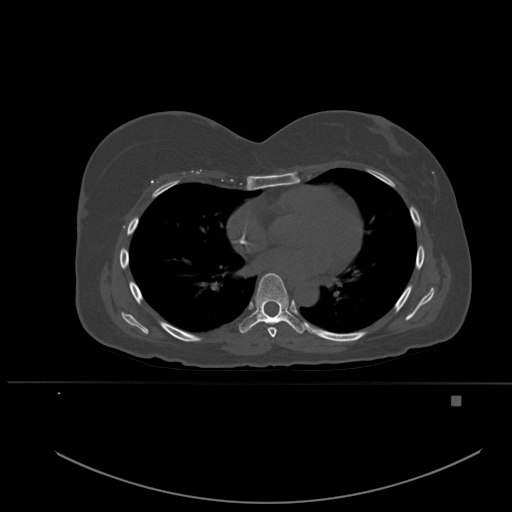
CT including the spine, one axial slice. Position 339 of 651 along the scan axis. Bone window (W 1800 / L 400 HU). 1.5 mm slice thickness. 512 × 512 image matrix, field of view 443 × 443 mm. Female patient, age 49 years. From the clinical record (not read from this slice): primary cancer: breast; vertebrae with lytic lesions (as recorded): L3, T12, L4.
Outlined on this slice (semi-automatically segmented with operator editing):
- T6 vertebra: bounding box (x1, y1, x2, y2) in pixels: (268, 327, 277, 338)
- T7 vertebra: (239, 273, 306, 334)